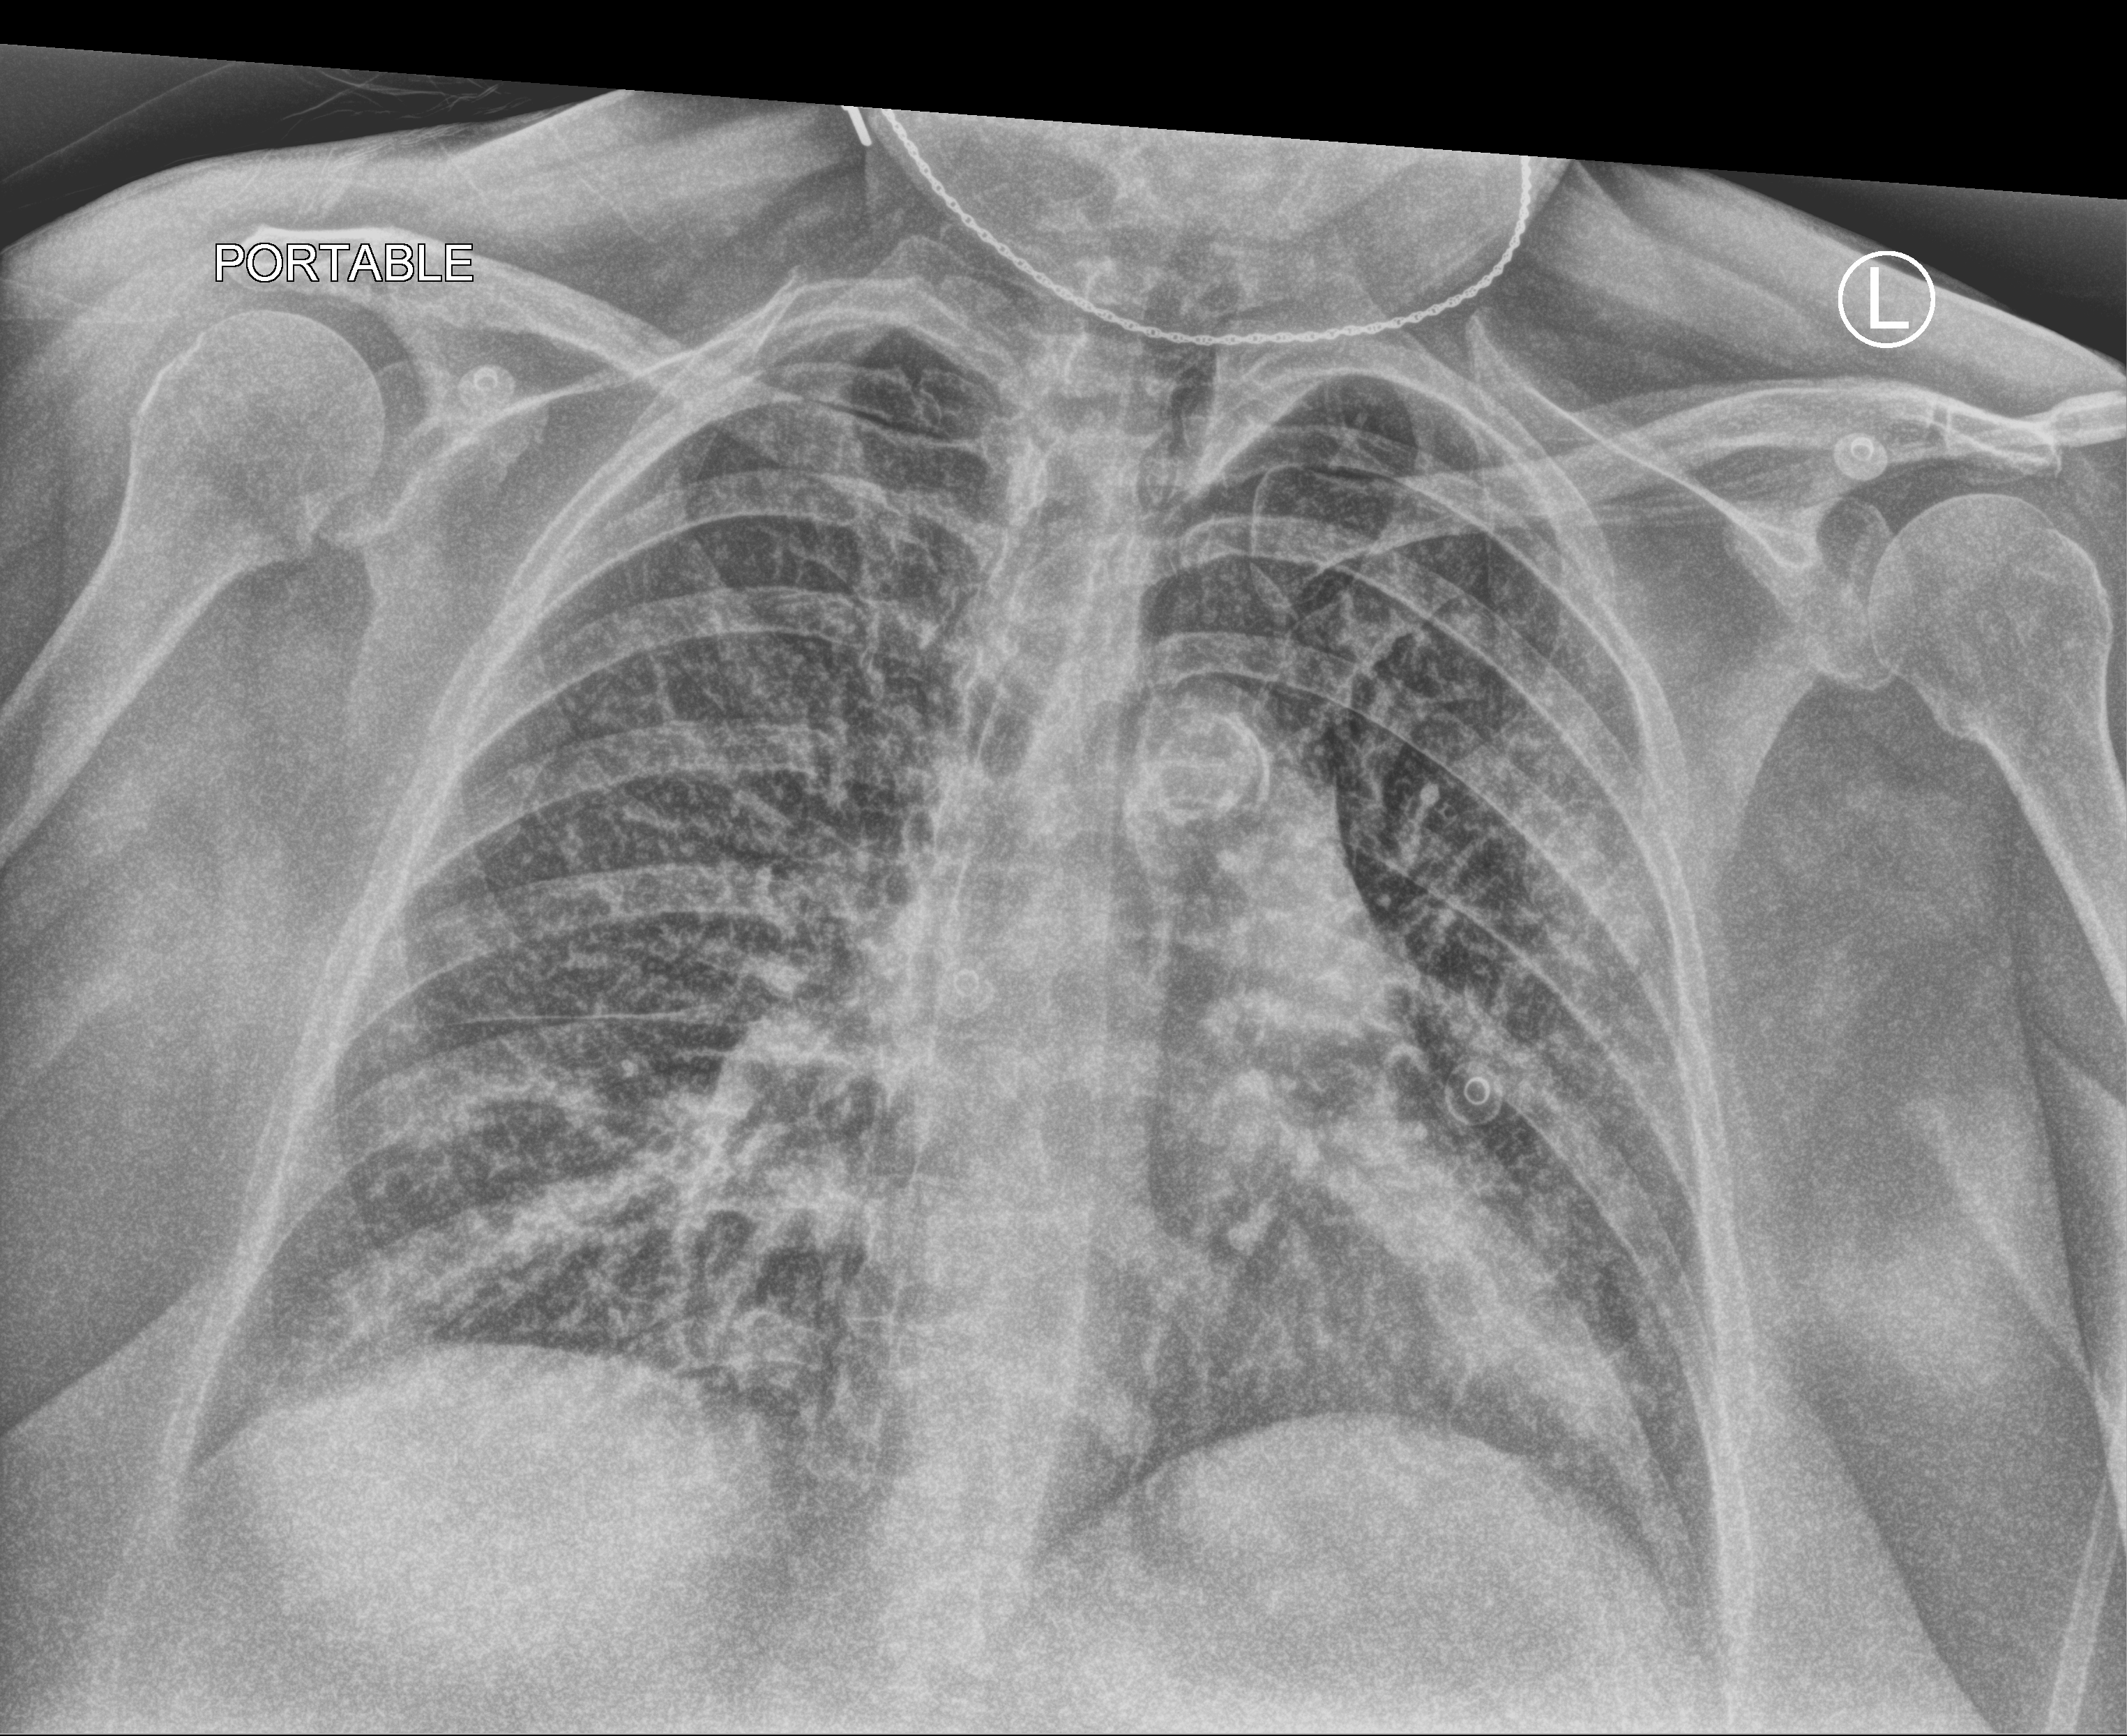
Bedside chest radiograph (computed radiography), anteroposterior (AP) projection. Female patient hospitalised with COVID-19, age 60–74 years.
Hospital-stay facts (about this admission, not read from this image; timing relative to this image not recorded): length of hospital stay: 20 days; mechanically ventilated during this hospital stay: no; admitted to intensive care during this hospital stay: no.